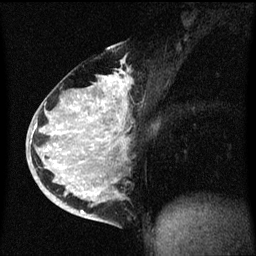
Breast MRI (dynamic contrast-enhanced), one sagittal slice. Dynamic contrast-enhanced series, image 2 of 3 at this slice position (ordered by acquisition). 1.5 T. TE 4.2 ms, TR 8.4 ms. 256 × 256 image matrix, field of view 200 × 200 mm. Patient: female, 34 years. Case-level facts recorded for this patient, not image findings: setting: breast cancer imaged before/during neoadjuvant chemotherapy; receptor status: HR-positive, HER2-negative.
Annotated regions visible in this slice (semi-automatic segmentation, software-assisted and operator-edited):
- analysis volume of interest (the breast-tissue region the enhancement analysis was run in; not a lesion): bounding box (x1, y1, x2, y2) in pixels: (34, 48, 133, 215)
- tumour enhancement mask (voxels above the 70 % enhancement threshold inside the analysis volume of interest): (34, 78, 121, 213)